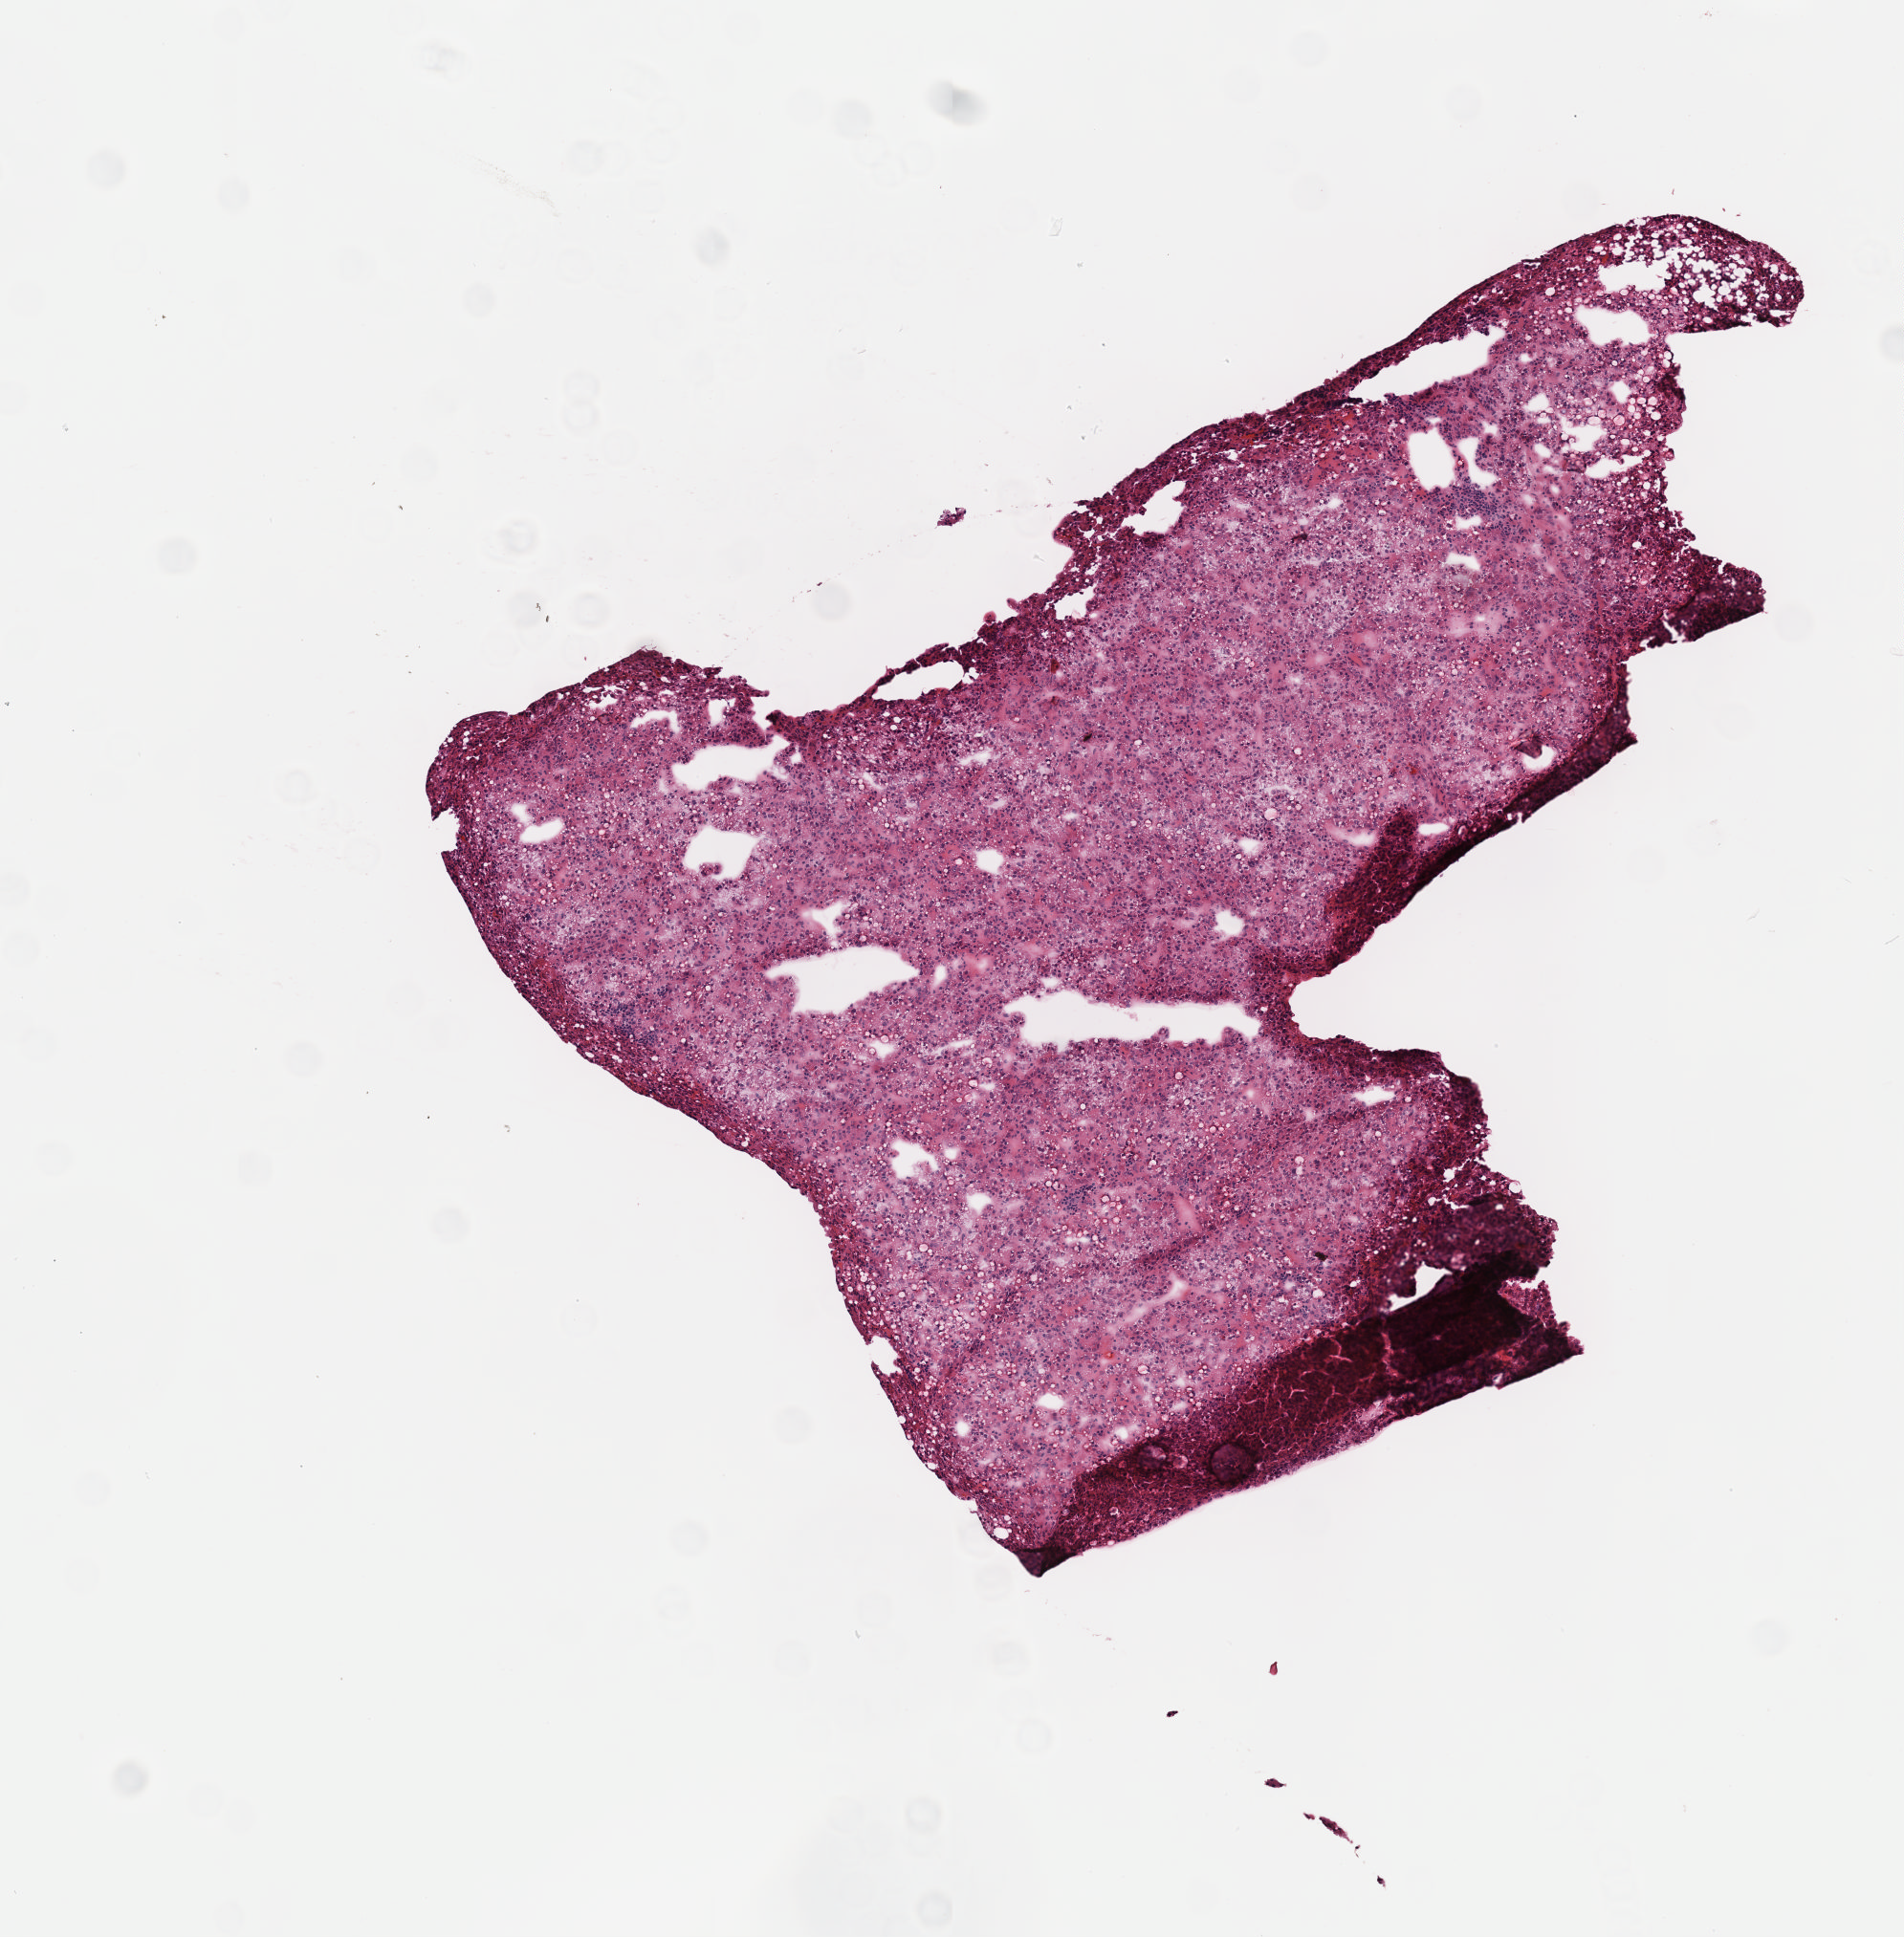
Digitized Hematoxylin and eosin (H&E) stained tissue section (whole slide), low-resolution overview of the scanned area, about 4.0 x 4.1 mm, frozen section, primary tumour sample from the liver. Male patient; age at initial diagnosis 51 years.
Histologic diagnosis: Hepatocellular carcinoma, NOS.